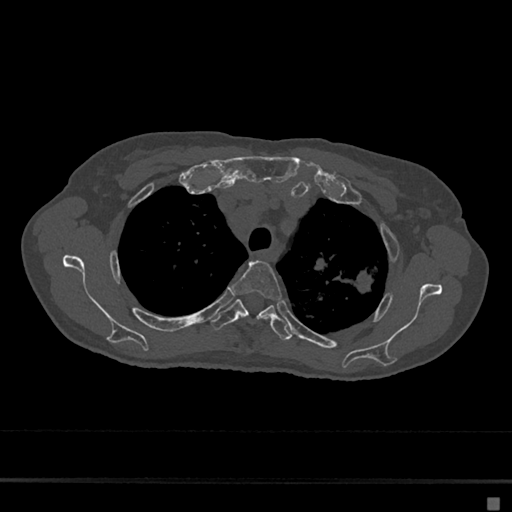
CT including the spine, one axial slice. Position 522 of 797 along the scan axis. 120 kVp. Bone window (W 1800 / L 400 HU). 0.5 mm slice thickness. 512 × 512 image matrix, field of view 360 × 360 mm. Female patient, age 68 years. Case-level facts recorded for this patient, not image findings: primary cancer: renal.
Structures marked on this image (semi-automatically segmented with operator editing):
- T3 vertebra: box from (x=230, y=260) to (x=282, y=320) px
- T4 vertebra: (x=210, y=299)–(x=292, y=341)